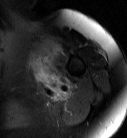
MRI of an extremity soft-tissue mass, one axial slice; position 61 of 87 along the scan axis; T2-weighted fat-saturated; MR volume resampled by the dataset authors to the PET/CT grid (not the native acquisition matrix); 127 × 138 image matrix, field of view 124 × 135 mm. Female patient. Case-level facts recorded for this patient, not image findings: histological type: pleiomorphic leiomyosarcoma; grade: high; site of the primary tumour: left biceps.
Outlined on this slice (expert contour drawn on MRI and transferred to this co-registered scan by the dataset authors):
- gross tumour volume including surrounding oedema: box from (x=29, y=39) to (x=60, y=88) px
- gross tumour volume (mass): (x=31, y=43)–(x=57, y=69)